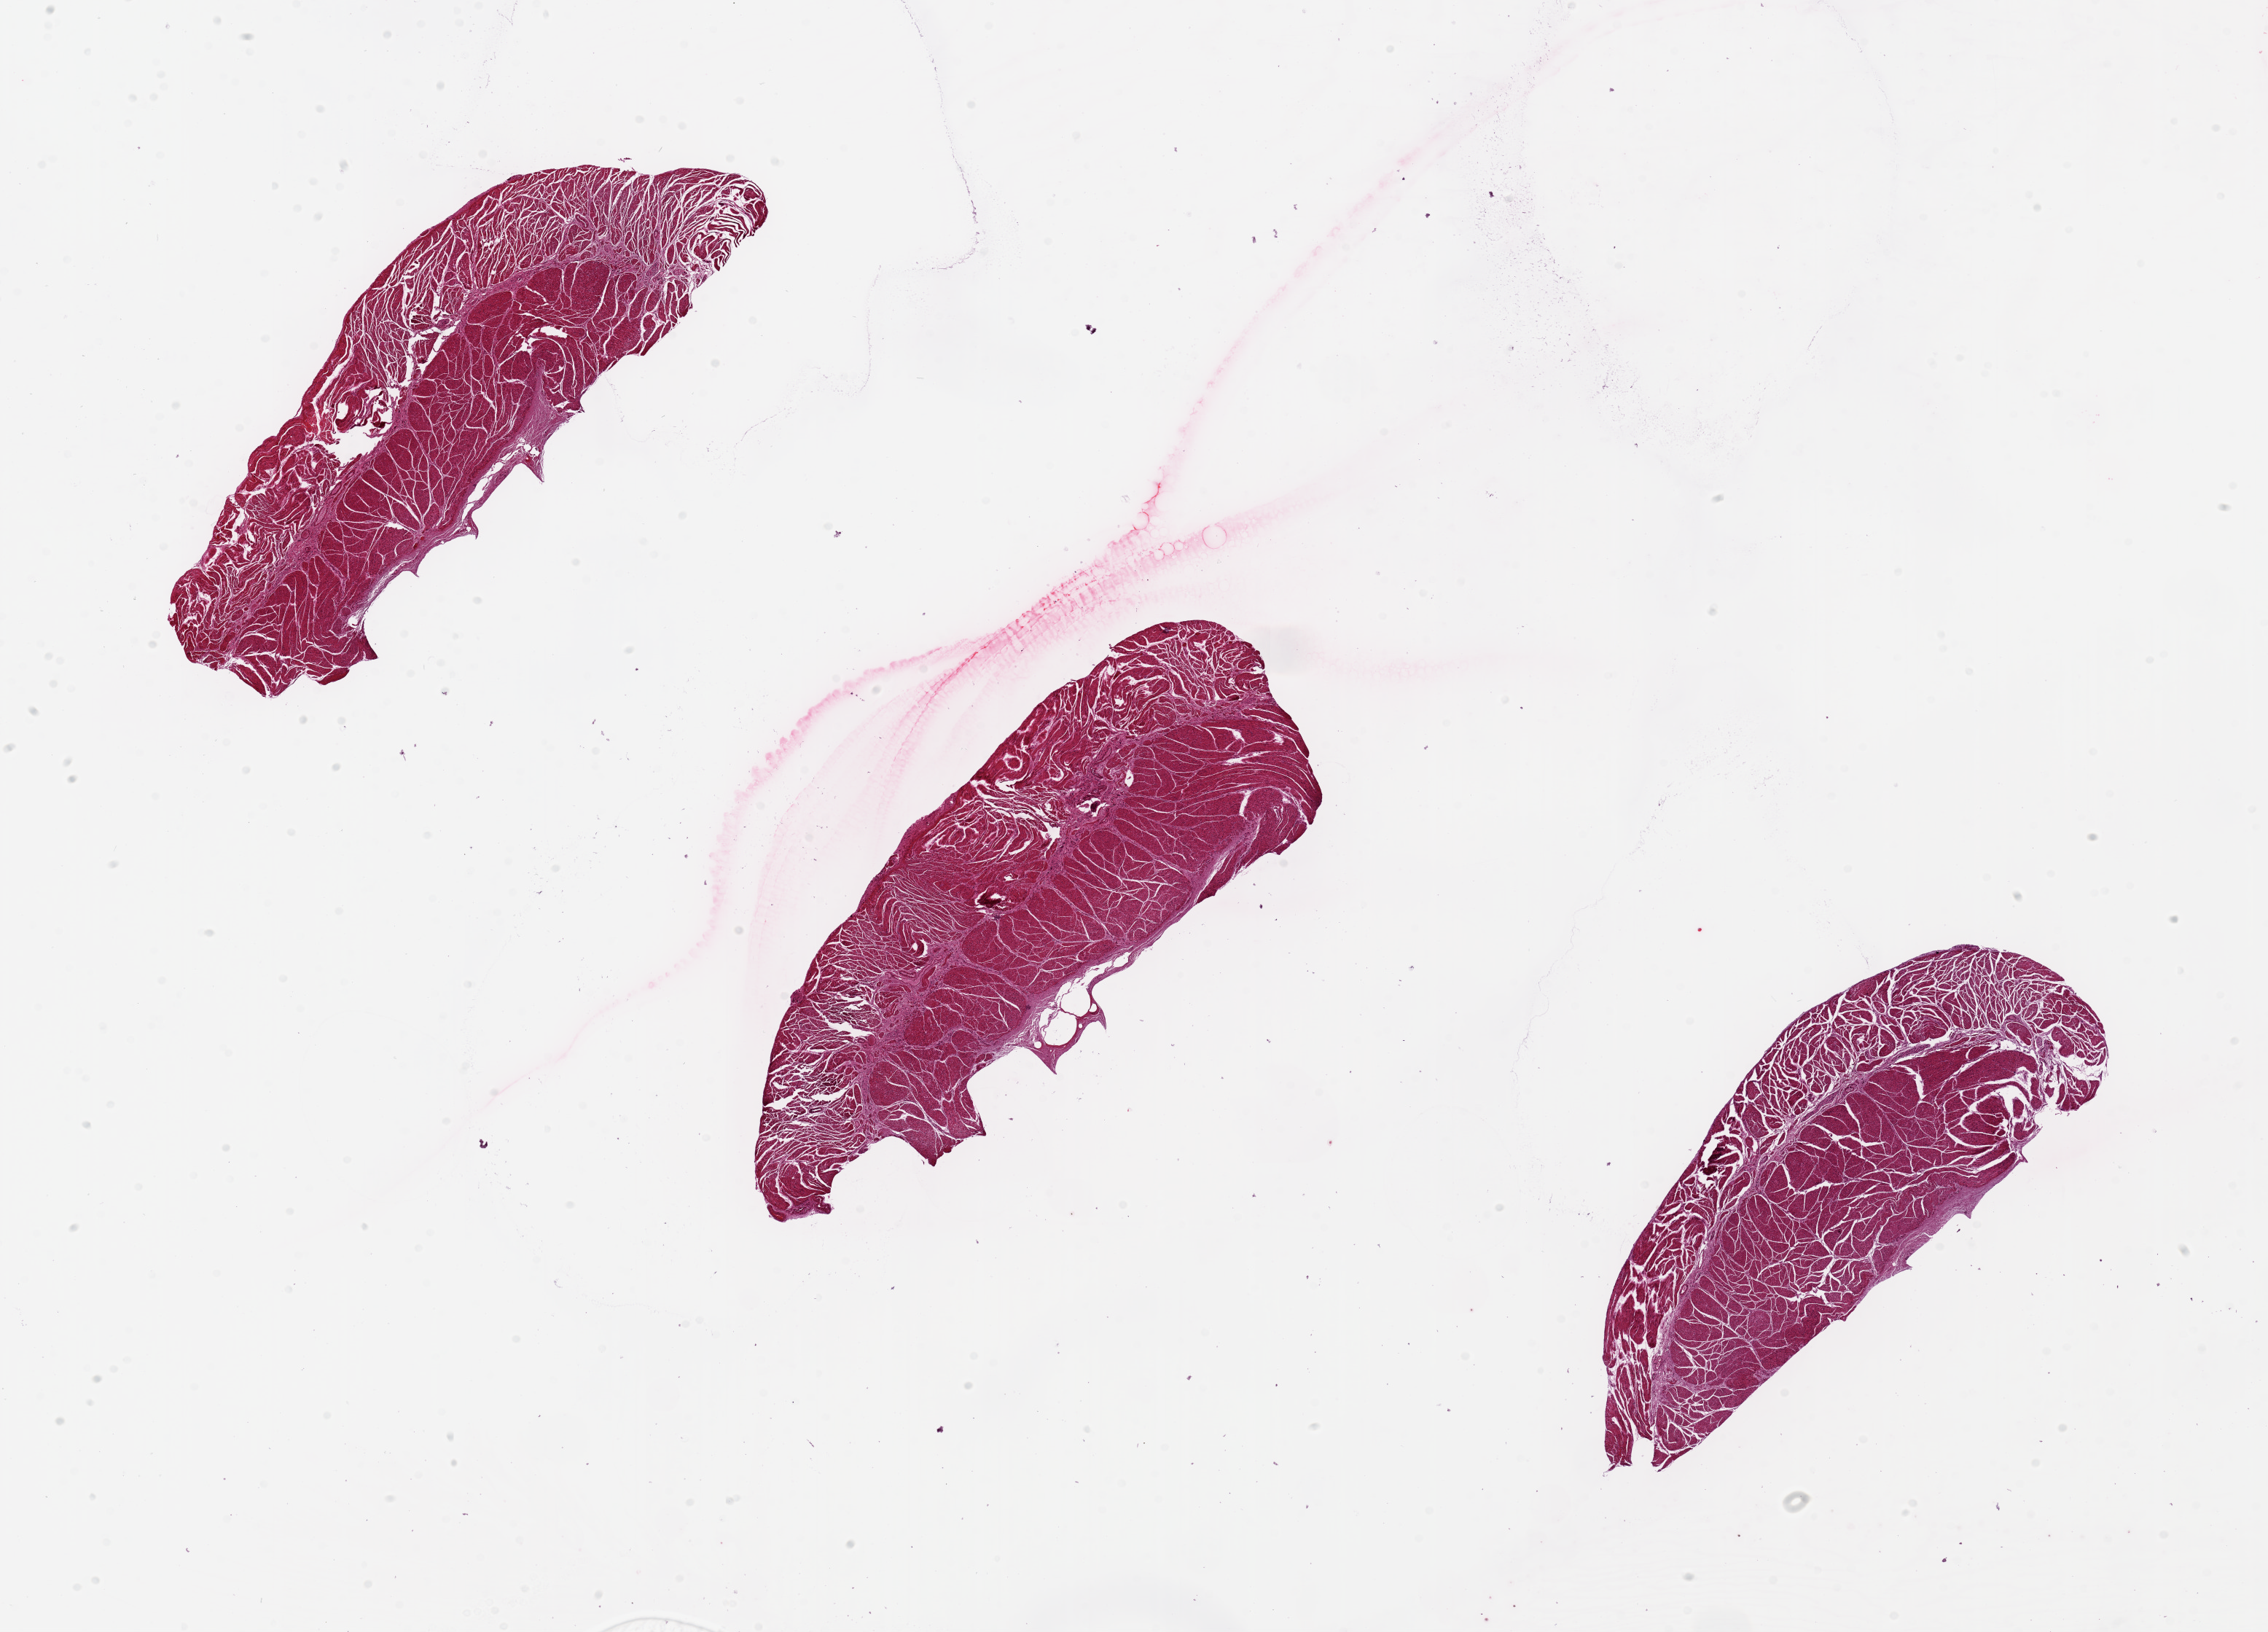
Whole-slide image, haematoxylin and eosin stain, brightfield, shown as a low-resolution overview of the whole scanned area (about 24.6 x 17.7 mm). PAXgene-fixed paraffin-embedded (PFPE) section. Sampled site (target tissue): esophageal muscle. Donor tissue sample. Donor sex: female.
- pathologist's review note for this sample: 3 pieces